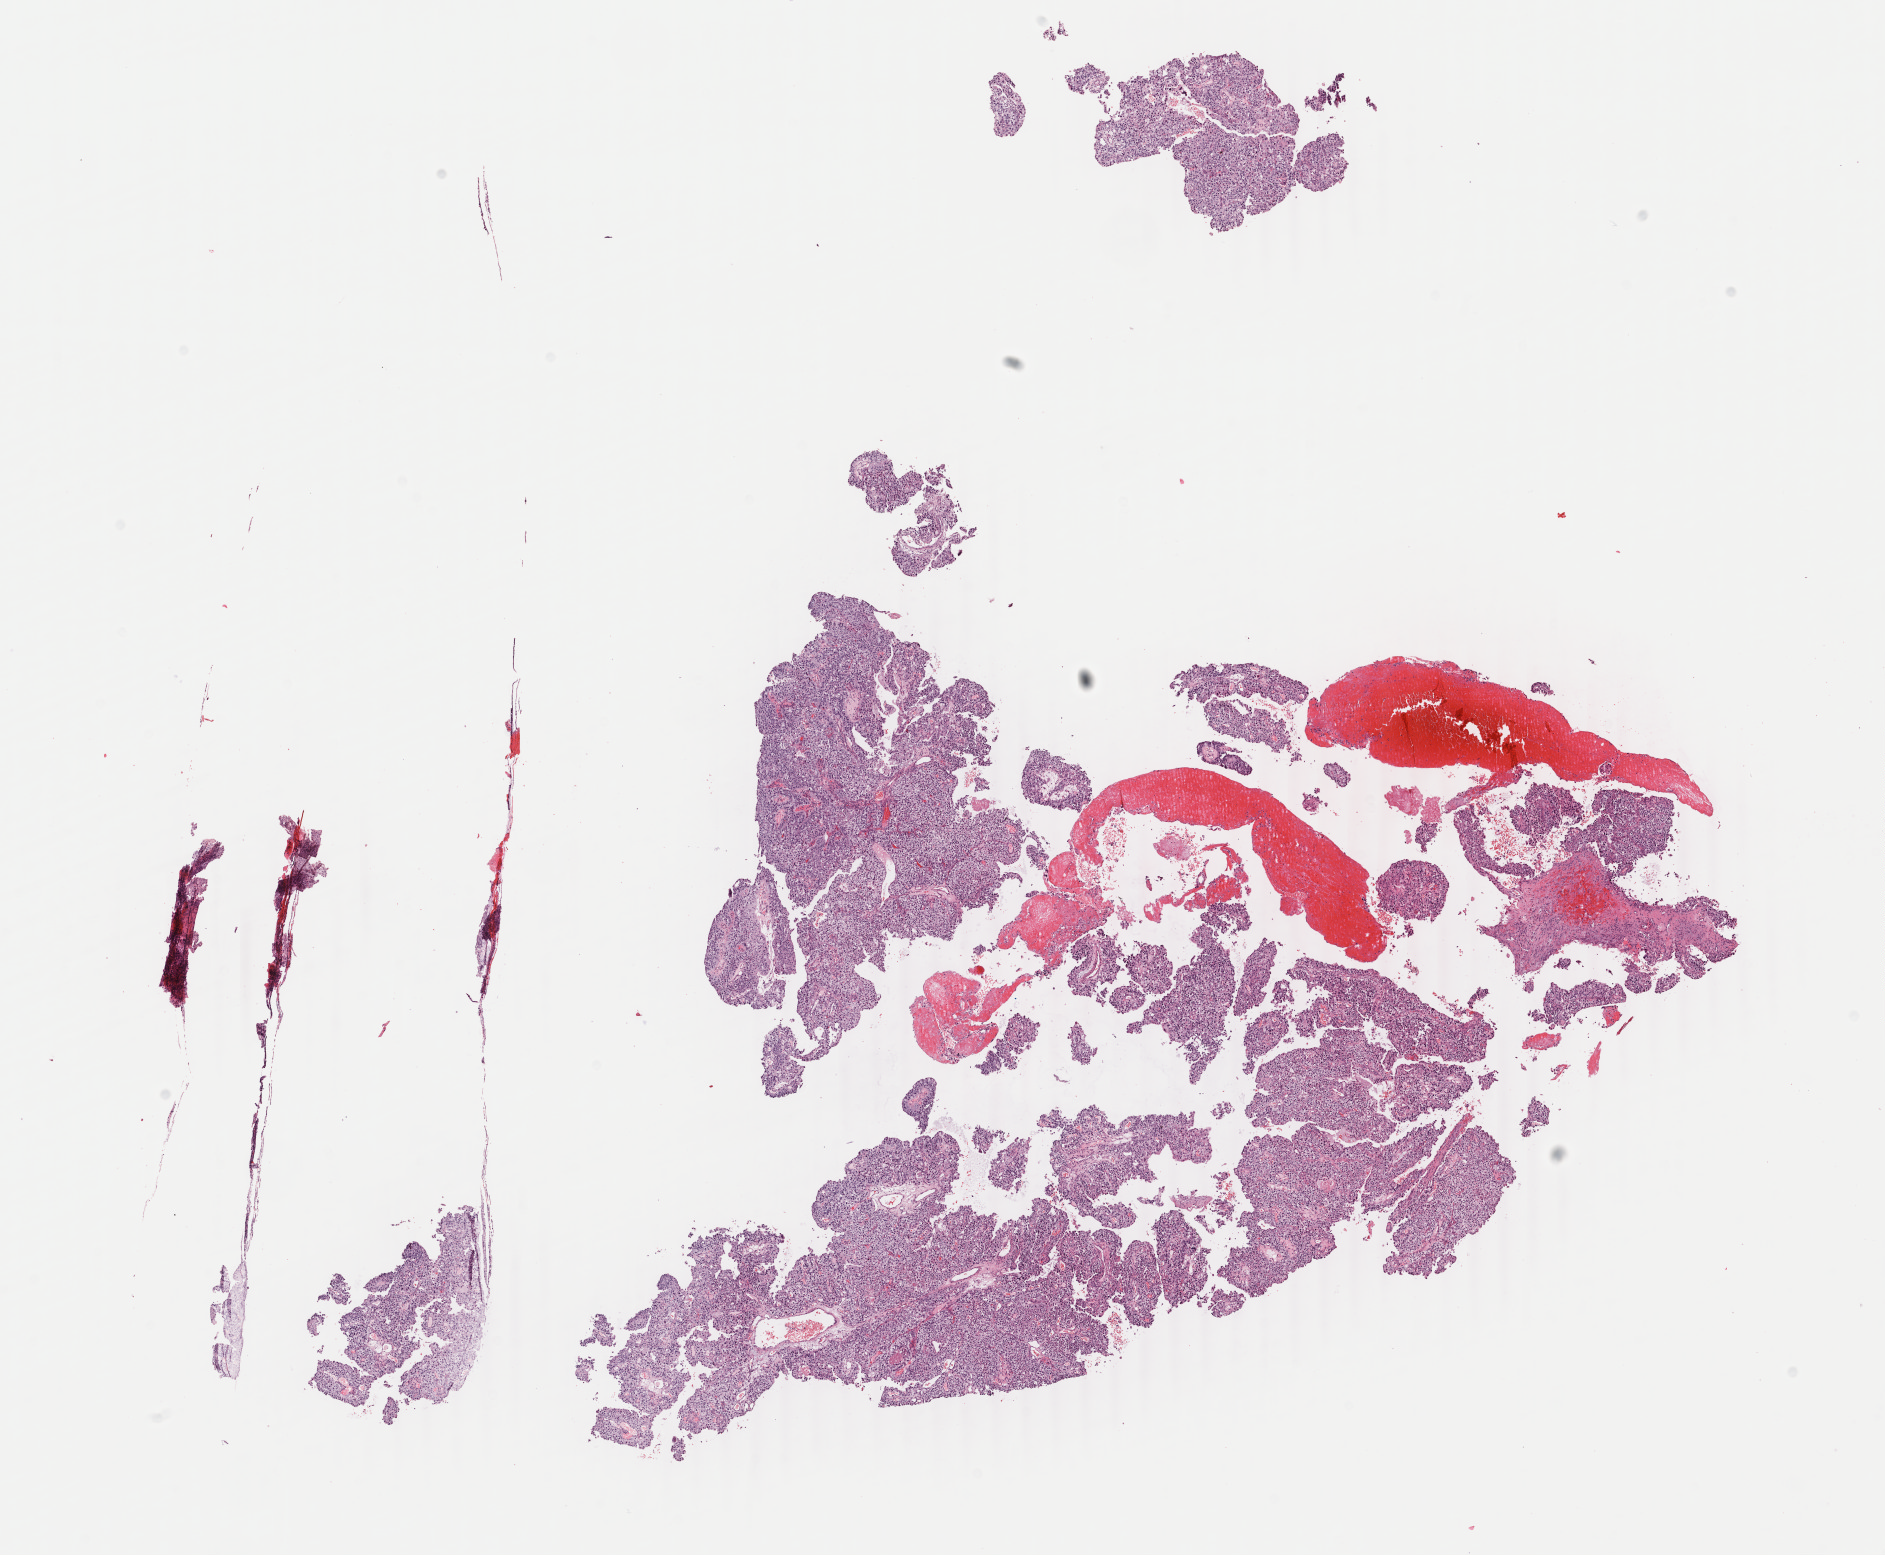
Digitized Hematoxylin and eosin (H&E) stained tissue section (whole slide), shown as a low-resolution overview of the whole scanned area (about 15.0 x 12.4 mm); frozen section from the bottom of the tissue portion; primary tumour sample from the bladder. Patient: male, age at initial diagnosis 73 years. Slide review estimates, as recorded: tumour cells 80%, tumour nuclei 95%, normal cells 0%, stromal cells 20%, necrosis 0%. Infiltration values recorded for this section: lymphocyte infiltration 0%, monocyte infiltration 0%, neutrophil infiltration 0%.
Pathologic diagnosis: Transitional cell carcinoma (dome of bladder). AJCC pathologic stage: I.